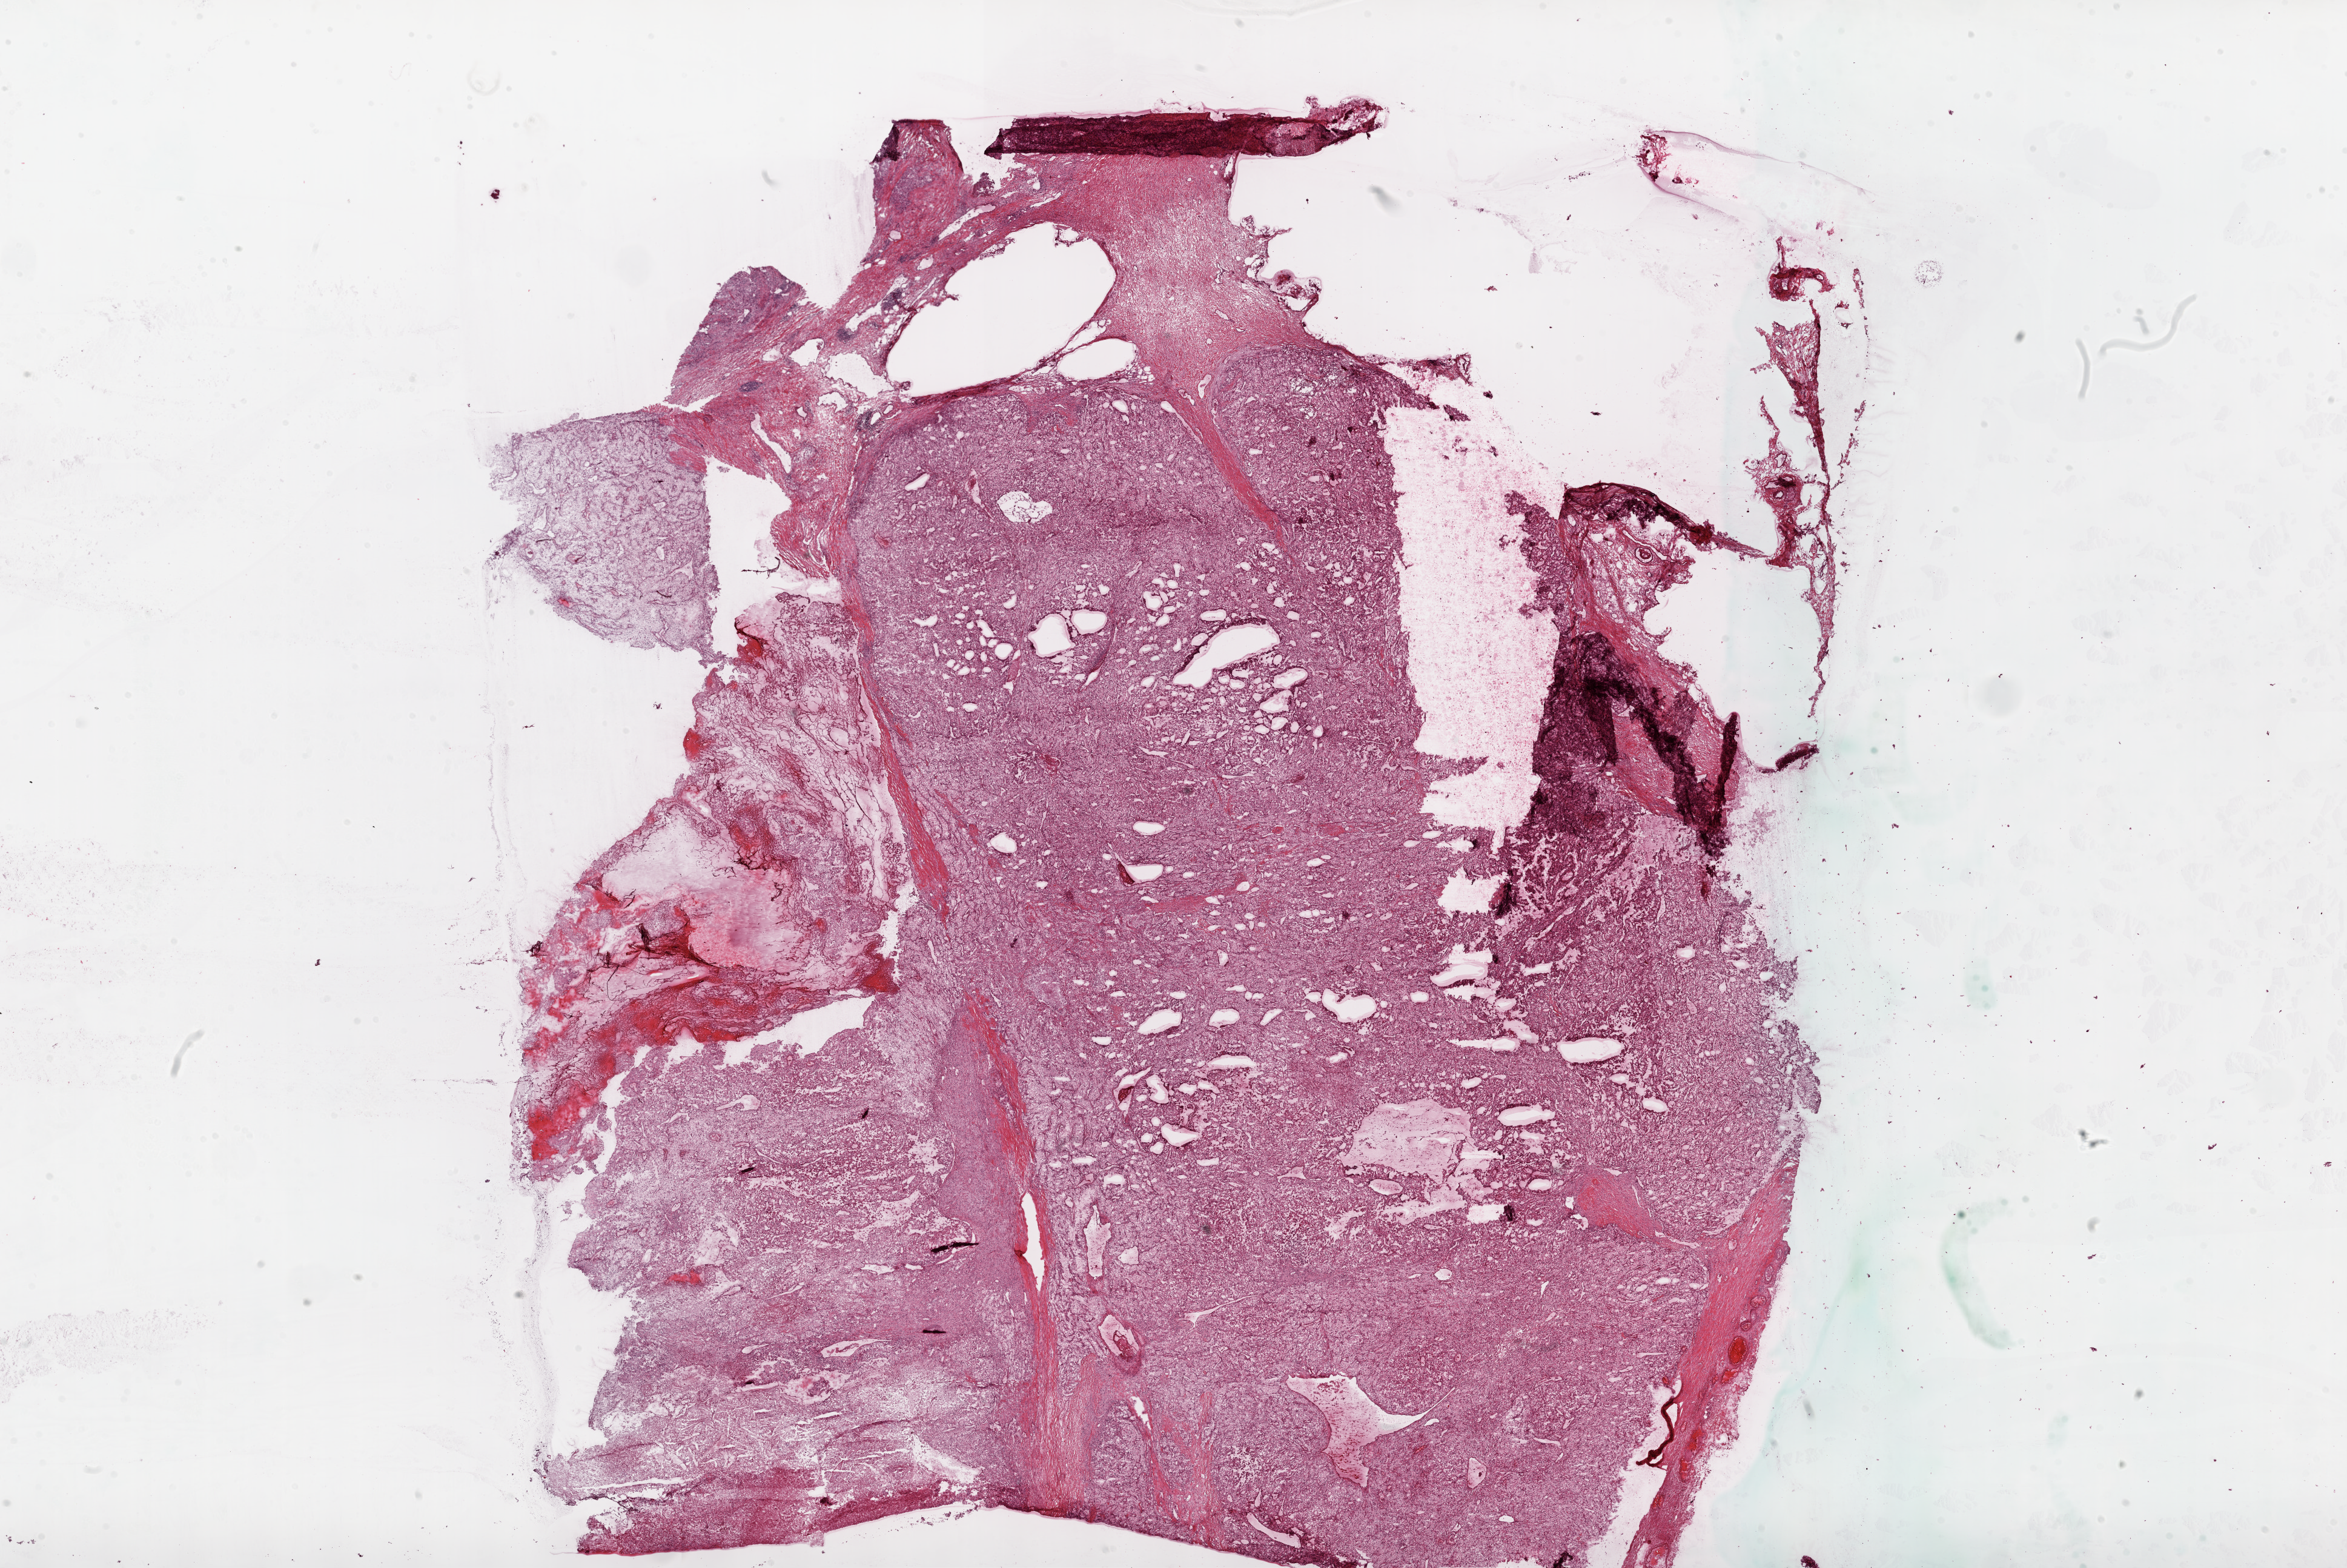
Whole-slide histology image, H&E-stained, whole scanned area (about 31.1 x 20.8 mm) shown as a low-resolution overview, frozen section from the top of the tissue portion, sample: primary tumour, kidney. Female, age 59 years at initial diagnosis.
Pathologic diagnosis: Clear cell adenocarcinoma, NOS.